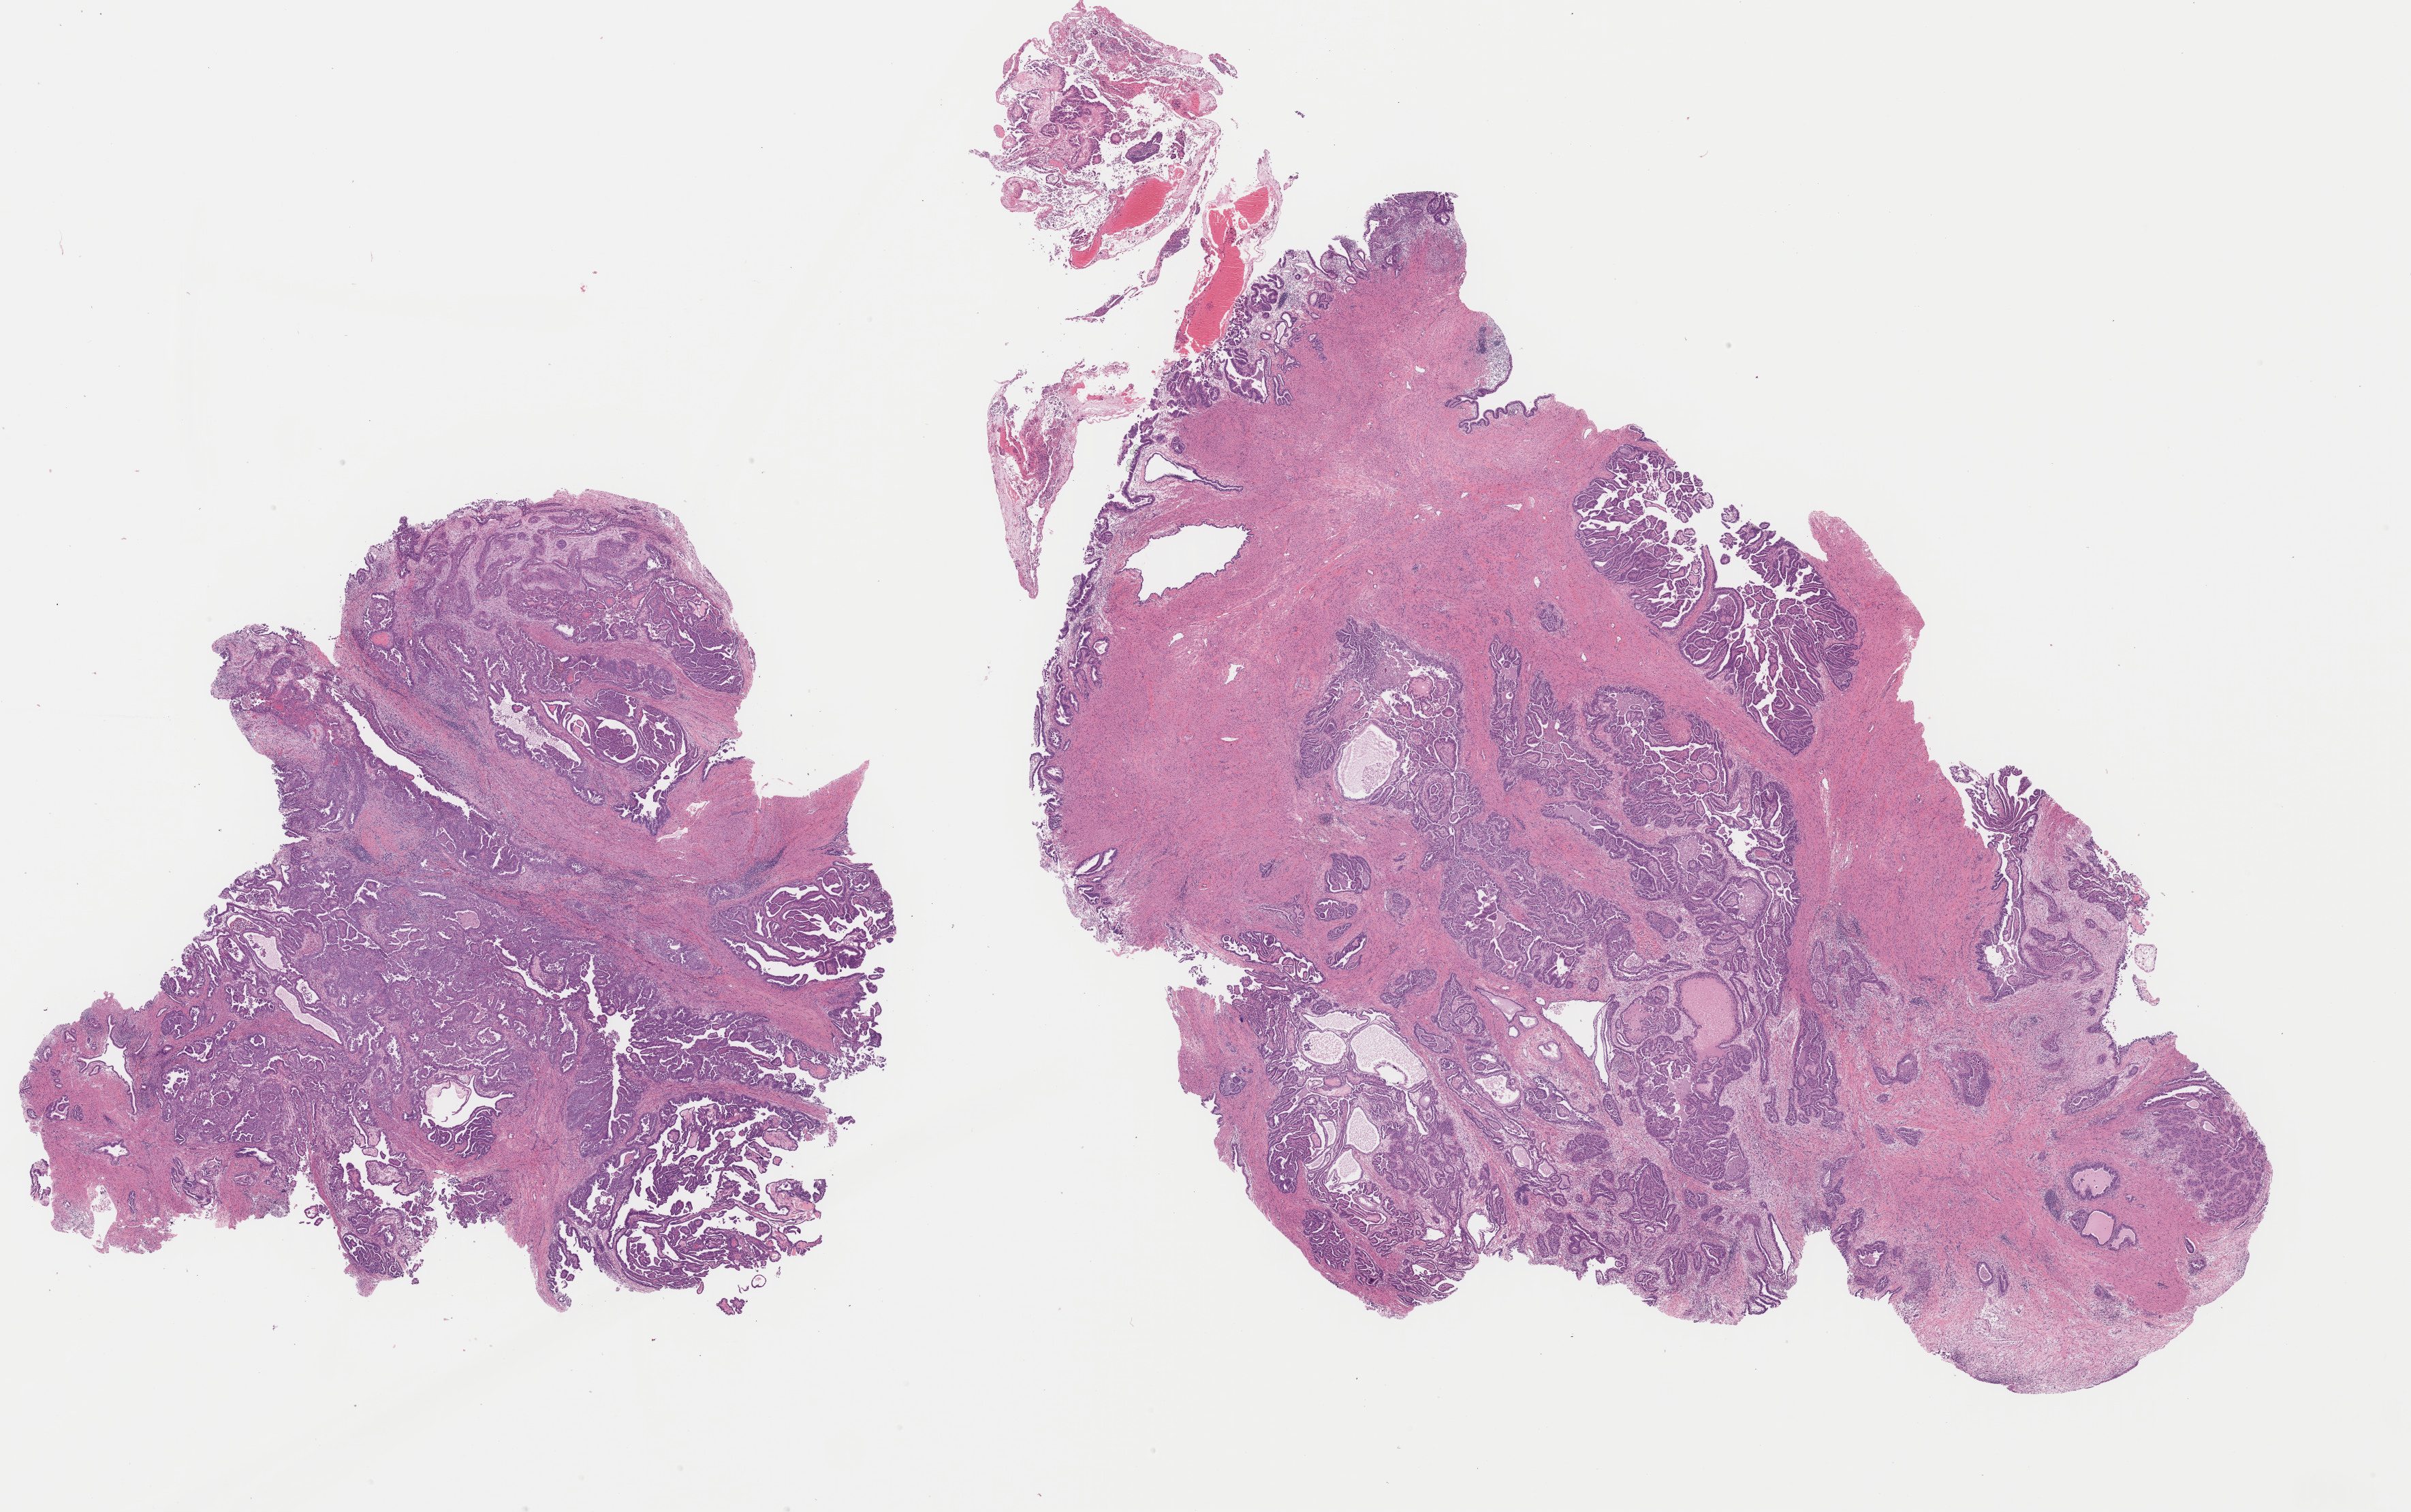
Whole-slide histology image, Hematoxylin and eosin (H&E) stained — whole scanned area (about 28.0 x 17.5 mm, from a 40x scan) shown as a low-resolution overview. Formalin-fixed paraffin-embedded (FFPE) diagnostic section. Primary tumour sample from the uterus. Female, age 77 years at initial diagnosis.
Pathologic diagnosis: Endometrioid adenocarcinoma, NOS (endometrium).